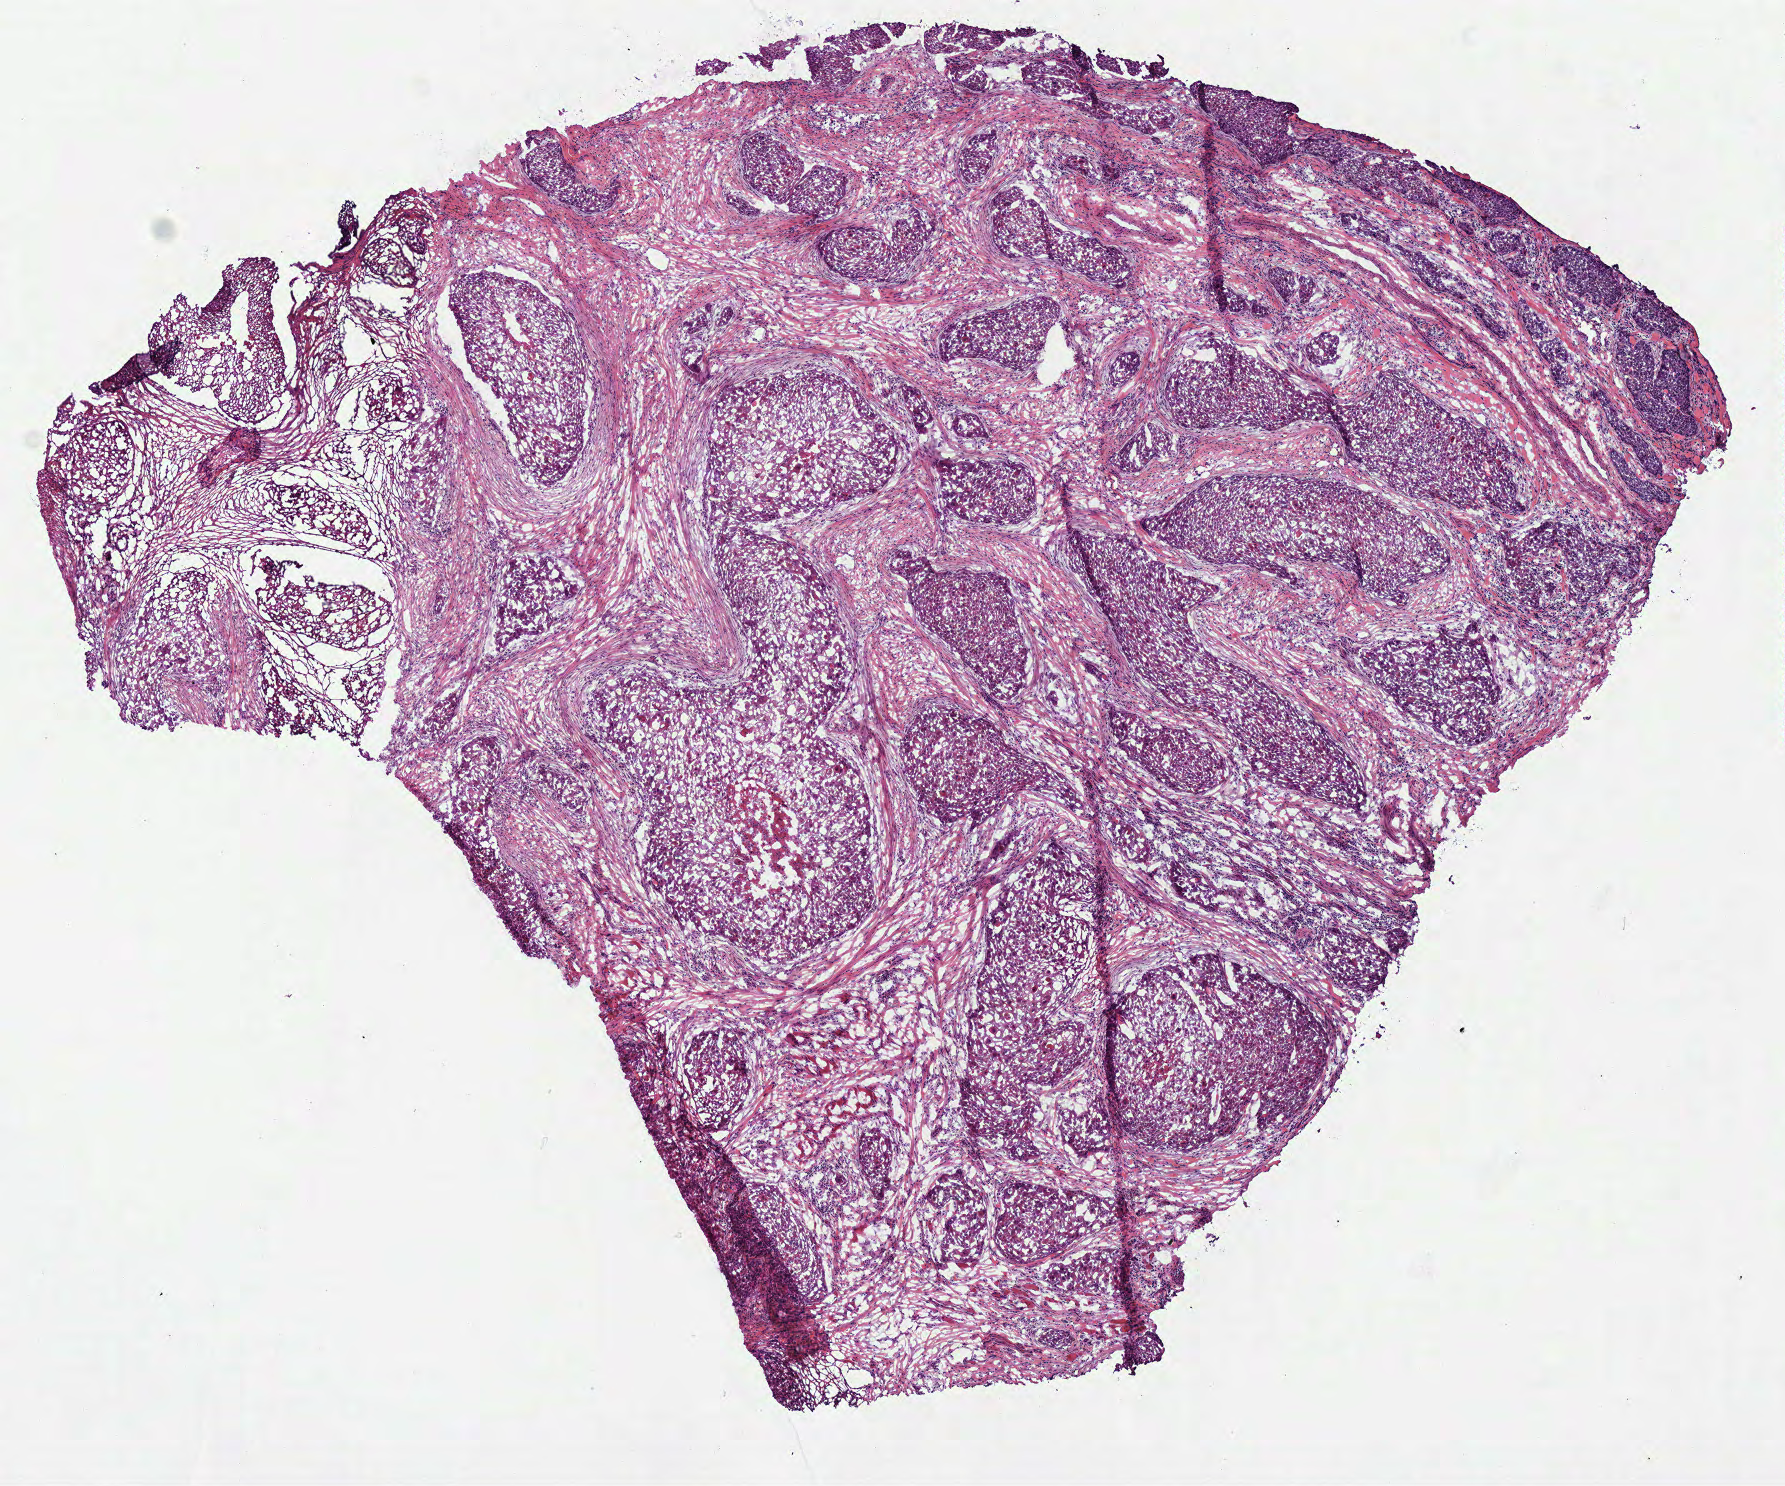
H&E whole-slide image, a low-resolution overview of the entire scanned area, about 7.0 x 5.9 mm (from a 40x scan), frozen section, sample: primary tumour, head and neck. Female patient; age at initial diagnosis 64 years. Histologic grade: G3 (poorly differentiated). Pathologist review of this section (percent, as recorded): tumour cells 50%, tumour nuclei 60%, normal cells 1%, stromal cells 48%, necrosis 1%. Infiltration values recorded for this section: lymphocyte infiltration 10%, monocyte infiltration 0%, neutrophil infiltration 0%.
Diagnosis: Squamous cell carcinoma, NOS (overlapping lesion of lip, oral cavity and pharynx). AJCC pathologic stage: IVA.